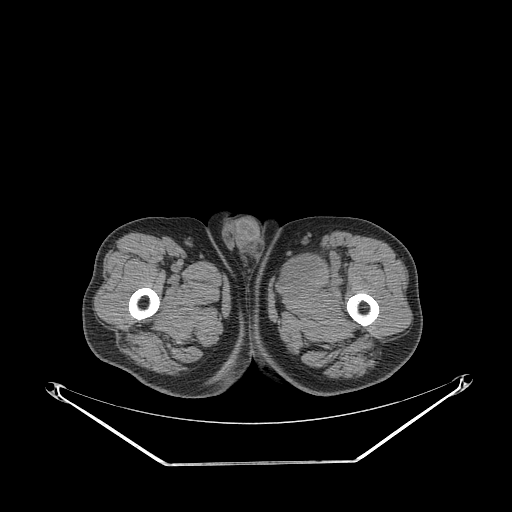
CT of an extremity soft-tissue mass (from a PET/CT study), one axial slice; slice 265 of 267 in the series (ordered by position); 140 kVp; soft-tissue window (W 400 / L 40 HU); 3.75 mm slice thickness; 512 × 512 image matrix, field of view 500 × 500 mm. Male patient. From the clinical record (not read from this slice): histological type: pleiomorphic liposarcoma; grade: high; site of the primary tumour: left thigh.
Annotated regions visible in this slice (expert contour drawn on MRI and transferred to this co-registered scan by the dataset authors):
- gross tumour volume including surrounding oedema: bounding box [x1, y1, x2, y2] px = [281, 246, 346, 291]
- gross tumour volume (mass): [281, 251, 323, 282]